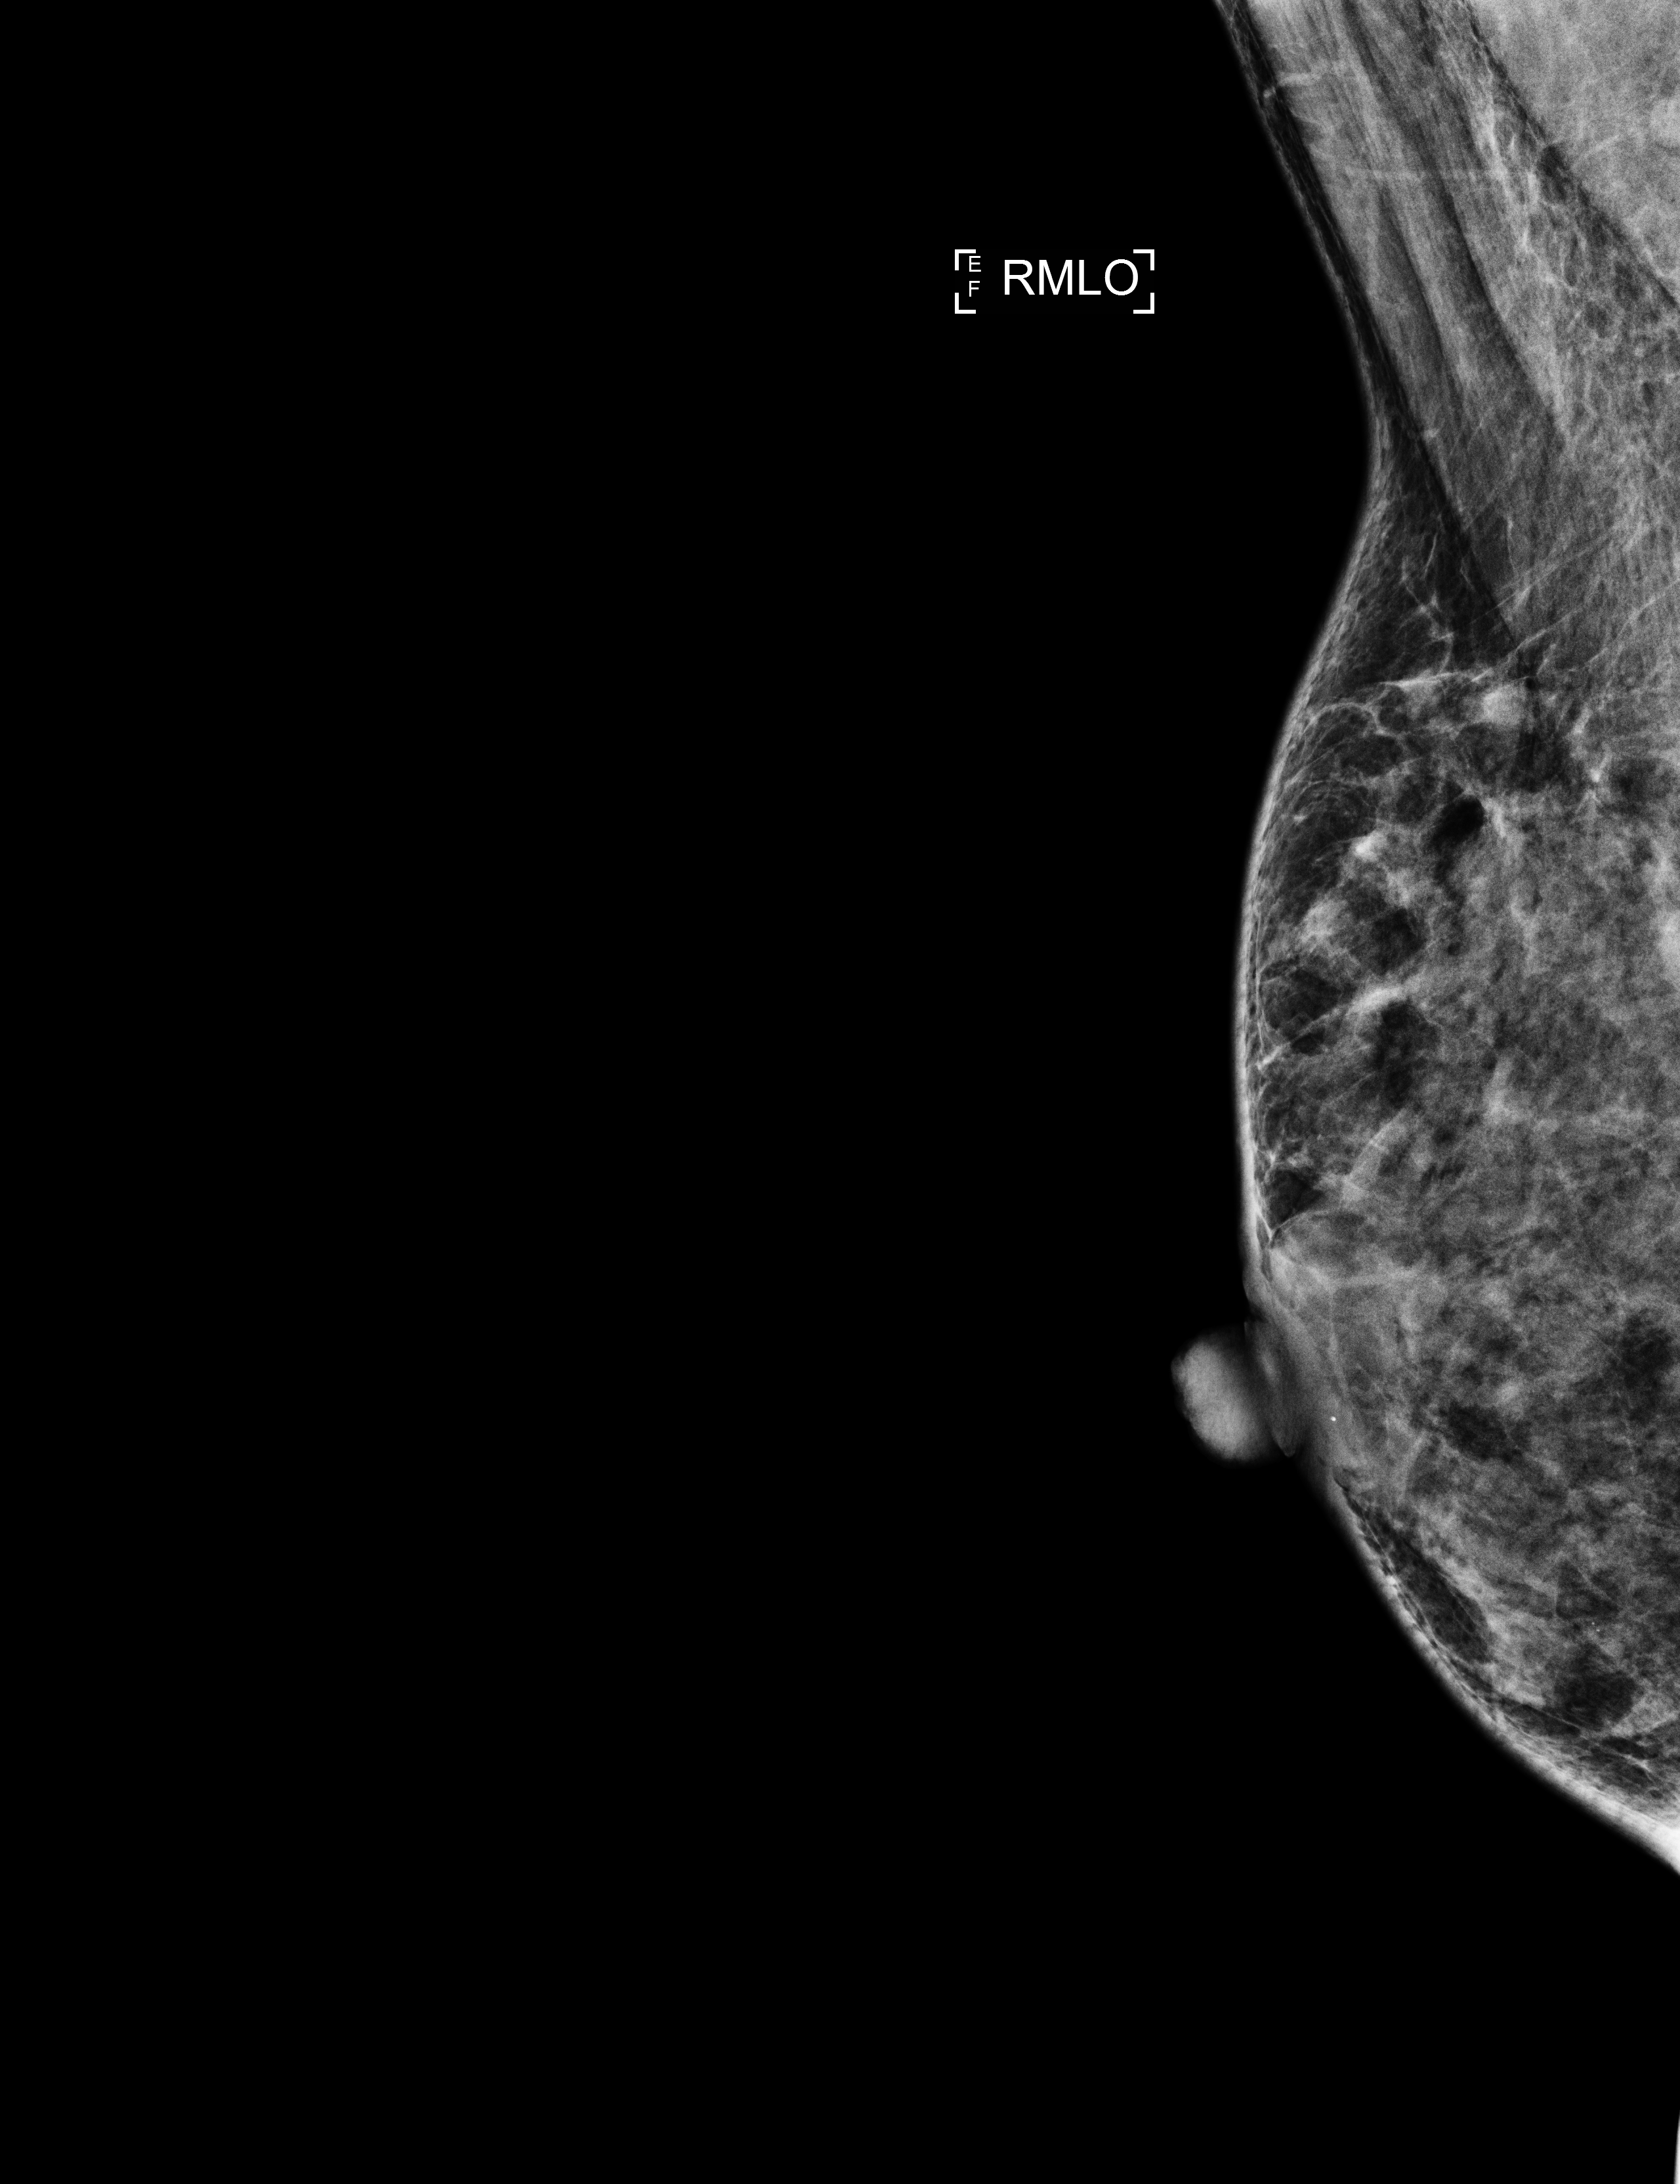
Digital mammogram (FFDM); right breast; medio-lateral oblique projection; screening examination. Patient aged 59 years (female).
Final BI-RADS assessment for this screening round (tomosynthesis exam, both breasts): category 2.